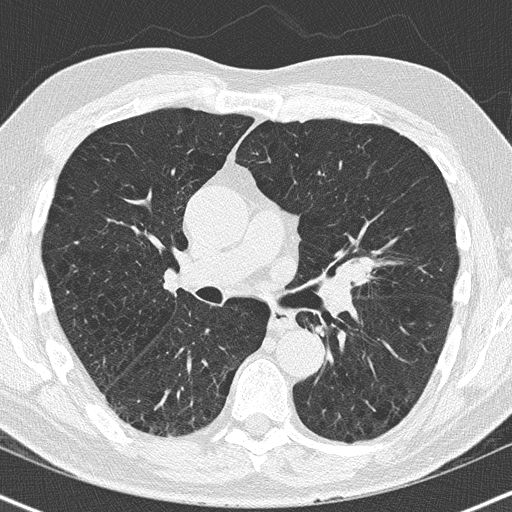
Low-dose screening chest CT, axial slice; first (baseline) screen; lung window (W 1500 / L -600 HU); 120 kVp; slice 74 of 163 in the series. Male, age 63 years at enrolment. Former smoker at enrolment.
- Expert-annotated lung lesion, bounding box (x1, y1, x2, y2) in pixels: (331, 252, 376, 290).
- The screening reader recorded 2 non-calcified nodules or masses ≥4 mm on this exam; which of them this box marks is not recorded.
- Later outcome: lung cancer diagnosed 32 days after this screen — squamous cell carcinoma, NOS, left upper lobe, moderately differentiated (G2), stage IA (AJCC 6th edition), 23 mm at pathology.